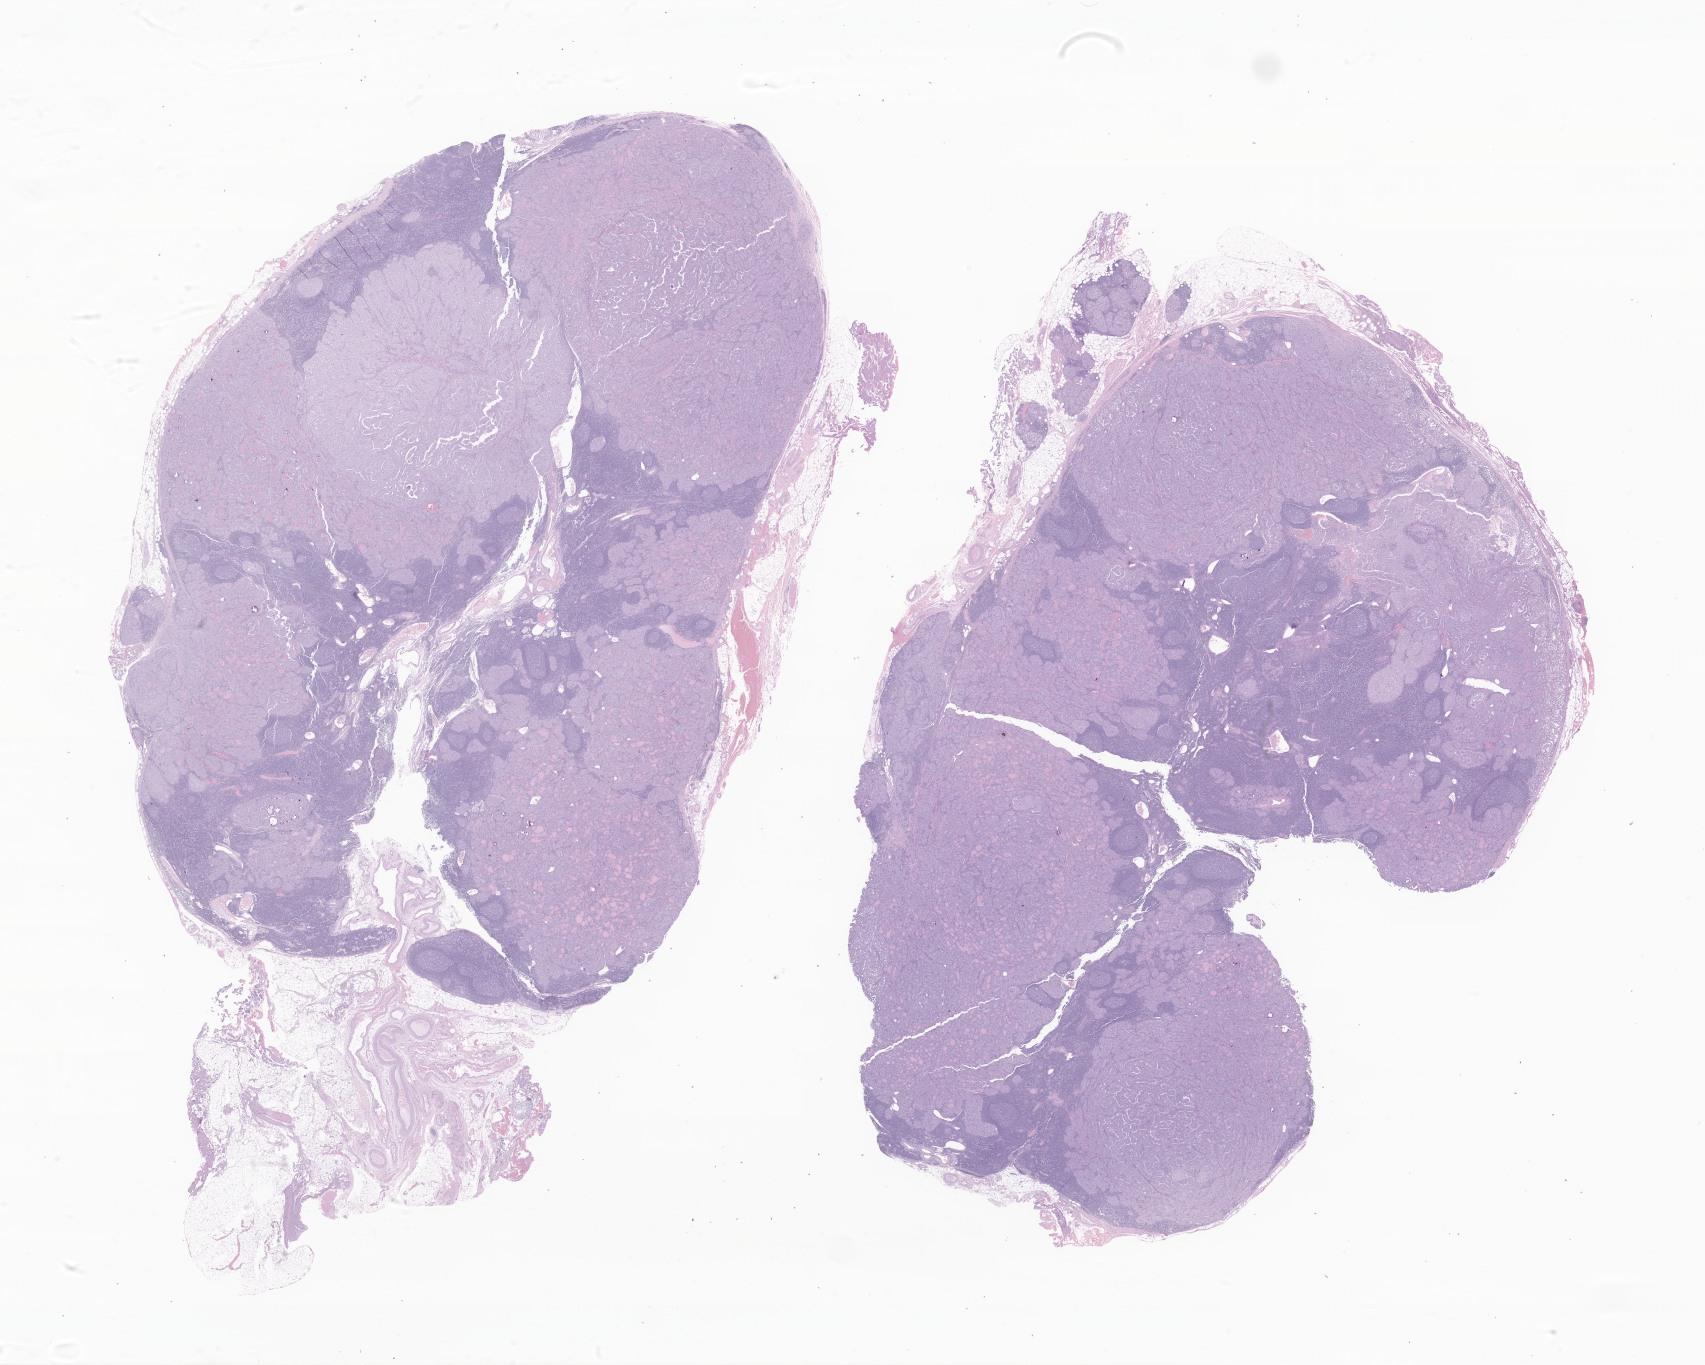
Digitized H&E-stained section of tumor tissue from the head and neck lymph node — shown as a low-resolution overview of the whole scanned area (about 28.8 x 23.0 mm), formalin-fixed paraffin-embedded section. Female patient, age 231 months (19 years 3 months).
Tissue or organ of origin (case record): lymph nodes of head, face and neck. Recorded diagnosis: Papillary carcinoma, NOS.